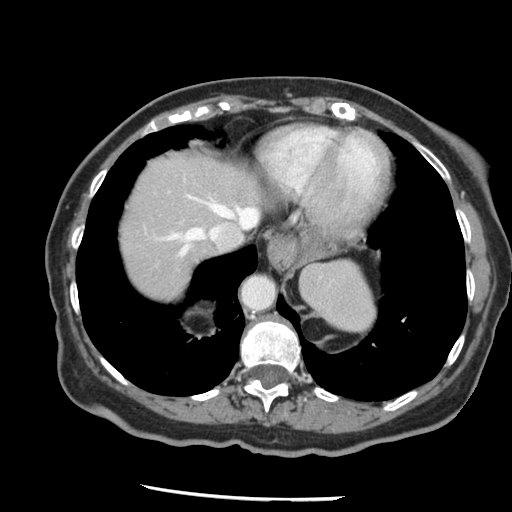
Contrast-enhanced abdominal CT, one axial slice; slice 115 of 148 in the series (ordered by position); reconstruction kernel STANDARD; intravenous contrast given; soft-tissue window (W 400 / L 40 HU); 2.5 mm slice thickness; 512 × 512 image matrix, field of view 330 × 330 mm. Female patient, age 85 years. Case-level facts recorded for this patient, not image findings: diagnosis: colorectal cancer liver metastases, imaged before liver resection; multiple liver metastases: no; largest metastasis: 0.9 cm; disease in both lobes: no.
Outlined on this slice (manually delineated by an expert):
- hepatic veins: bounding box (x1, y1, x2, y2) in pixels: (166, 196, 258, 256)
- liver: (118, 151, 263, 302)
- planned liver remnant (the part of the liver to remain after resection): (118, 151, 263, 302)